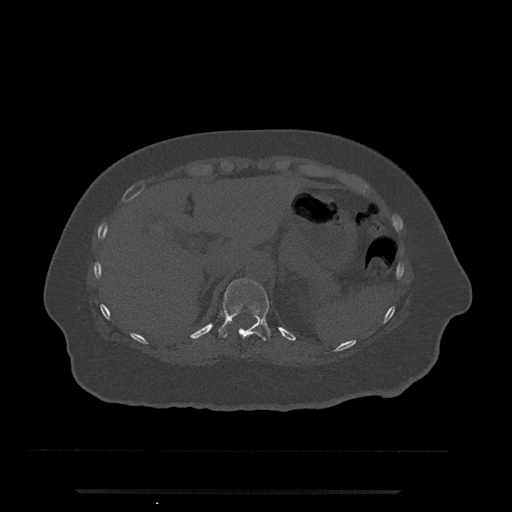
CT including the spine, one axial slice; position 230 of 797 along the scan axis; 120 kVp; bone window (W 1800 / L 400 HU); 0.5 mm slice thickness; 512 × 512 image matrix. Female patient, age 51 years. Case-level facts recorded for this patient, not image findings: primary cancer: neuro; vertebrae with lytic lesions (as recorded): T8.
Outlined on this slice (semi-automatic segmentation, software-assisted and operator-edited):
- T11 vertebra: bounding box <218,278,271,341> (left, top, right, bottom; pixels)